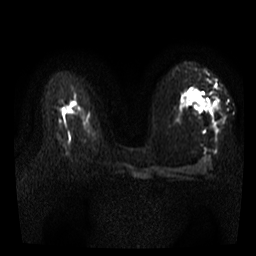
Breast MRI, one axial slice; position 20 of 35 along the scan axis; diffusion-weighted series; image 2 of 4 stored at this slice position (different b-values; order by instance number); 3 T; 5 mm slice thickness; 256 × 256 image matrix. Female patient.
Structures marked on this image (expert manual segmentation):
- tumour on diffusion-weighted imaging: bounding box (x1, y1, x2, y2) in pixels: (197, 102, 215, 109)